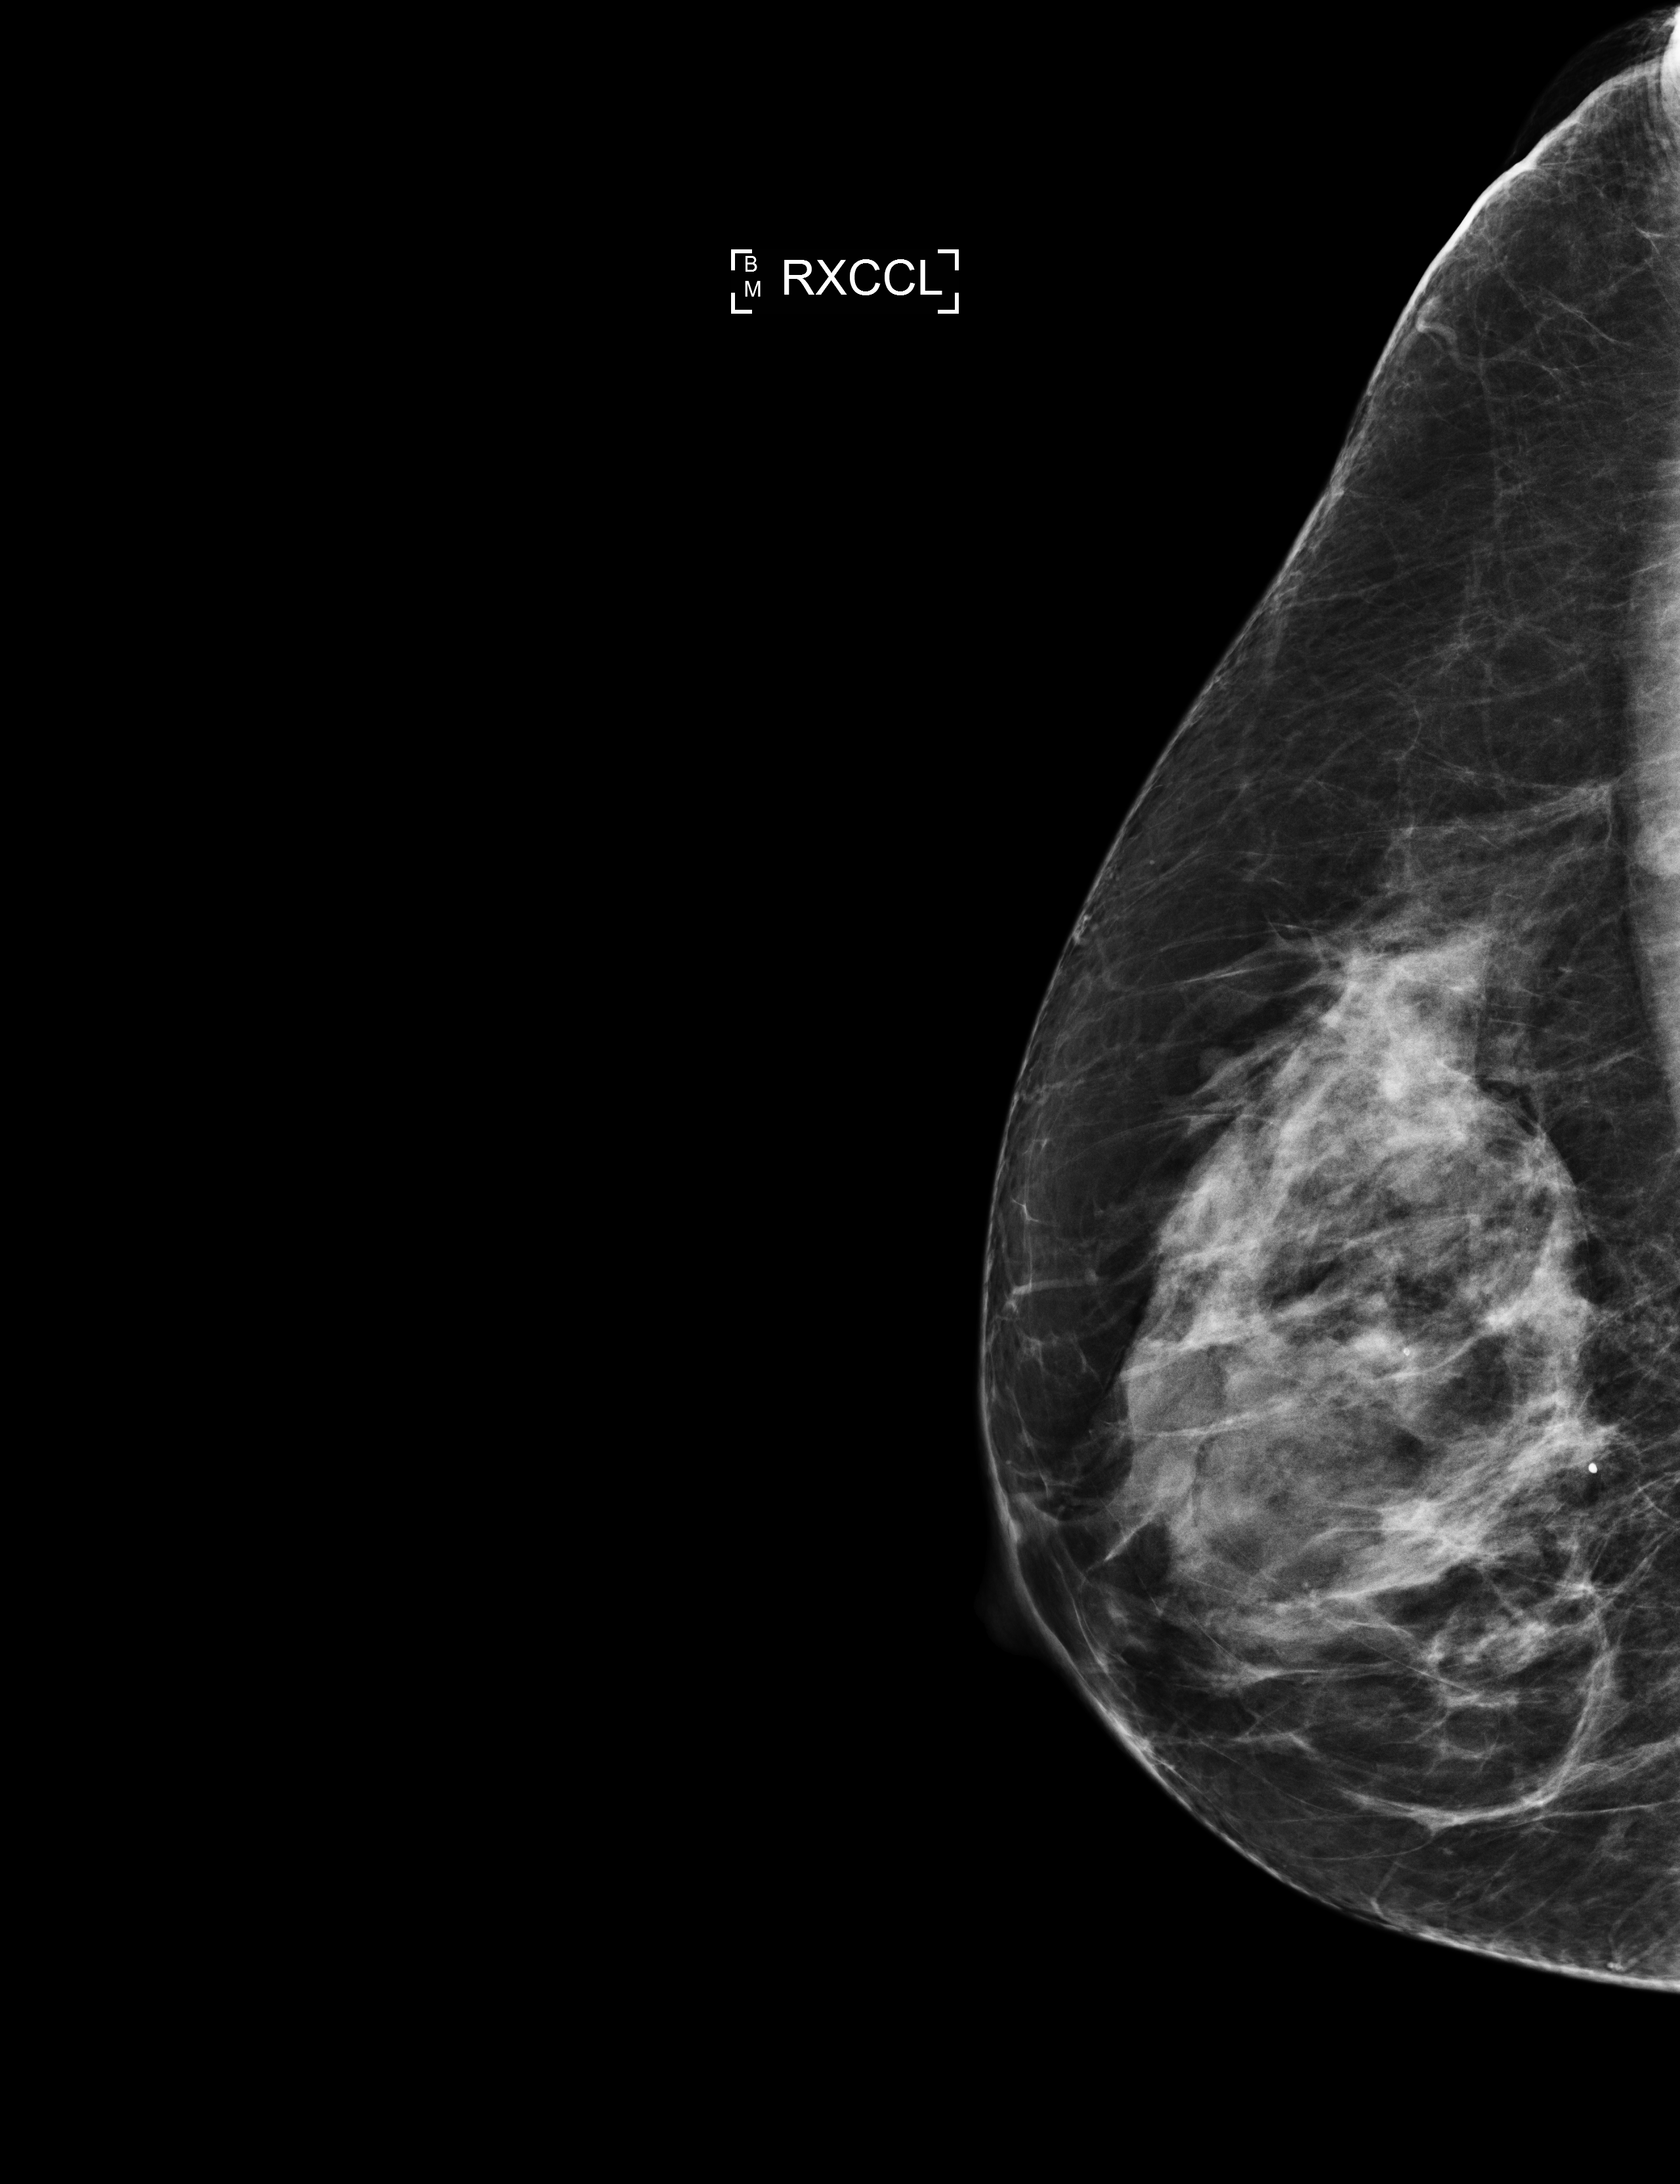
Screening examination; compressed breast thickness 54 mm; system: Selenia Dimensions. Patient aged 60 years (female).
Image type: full-field digital mammogram. Breast: right. Projection: exaggerated CC view (lateral).